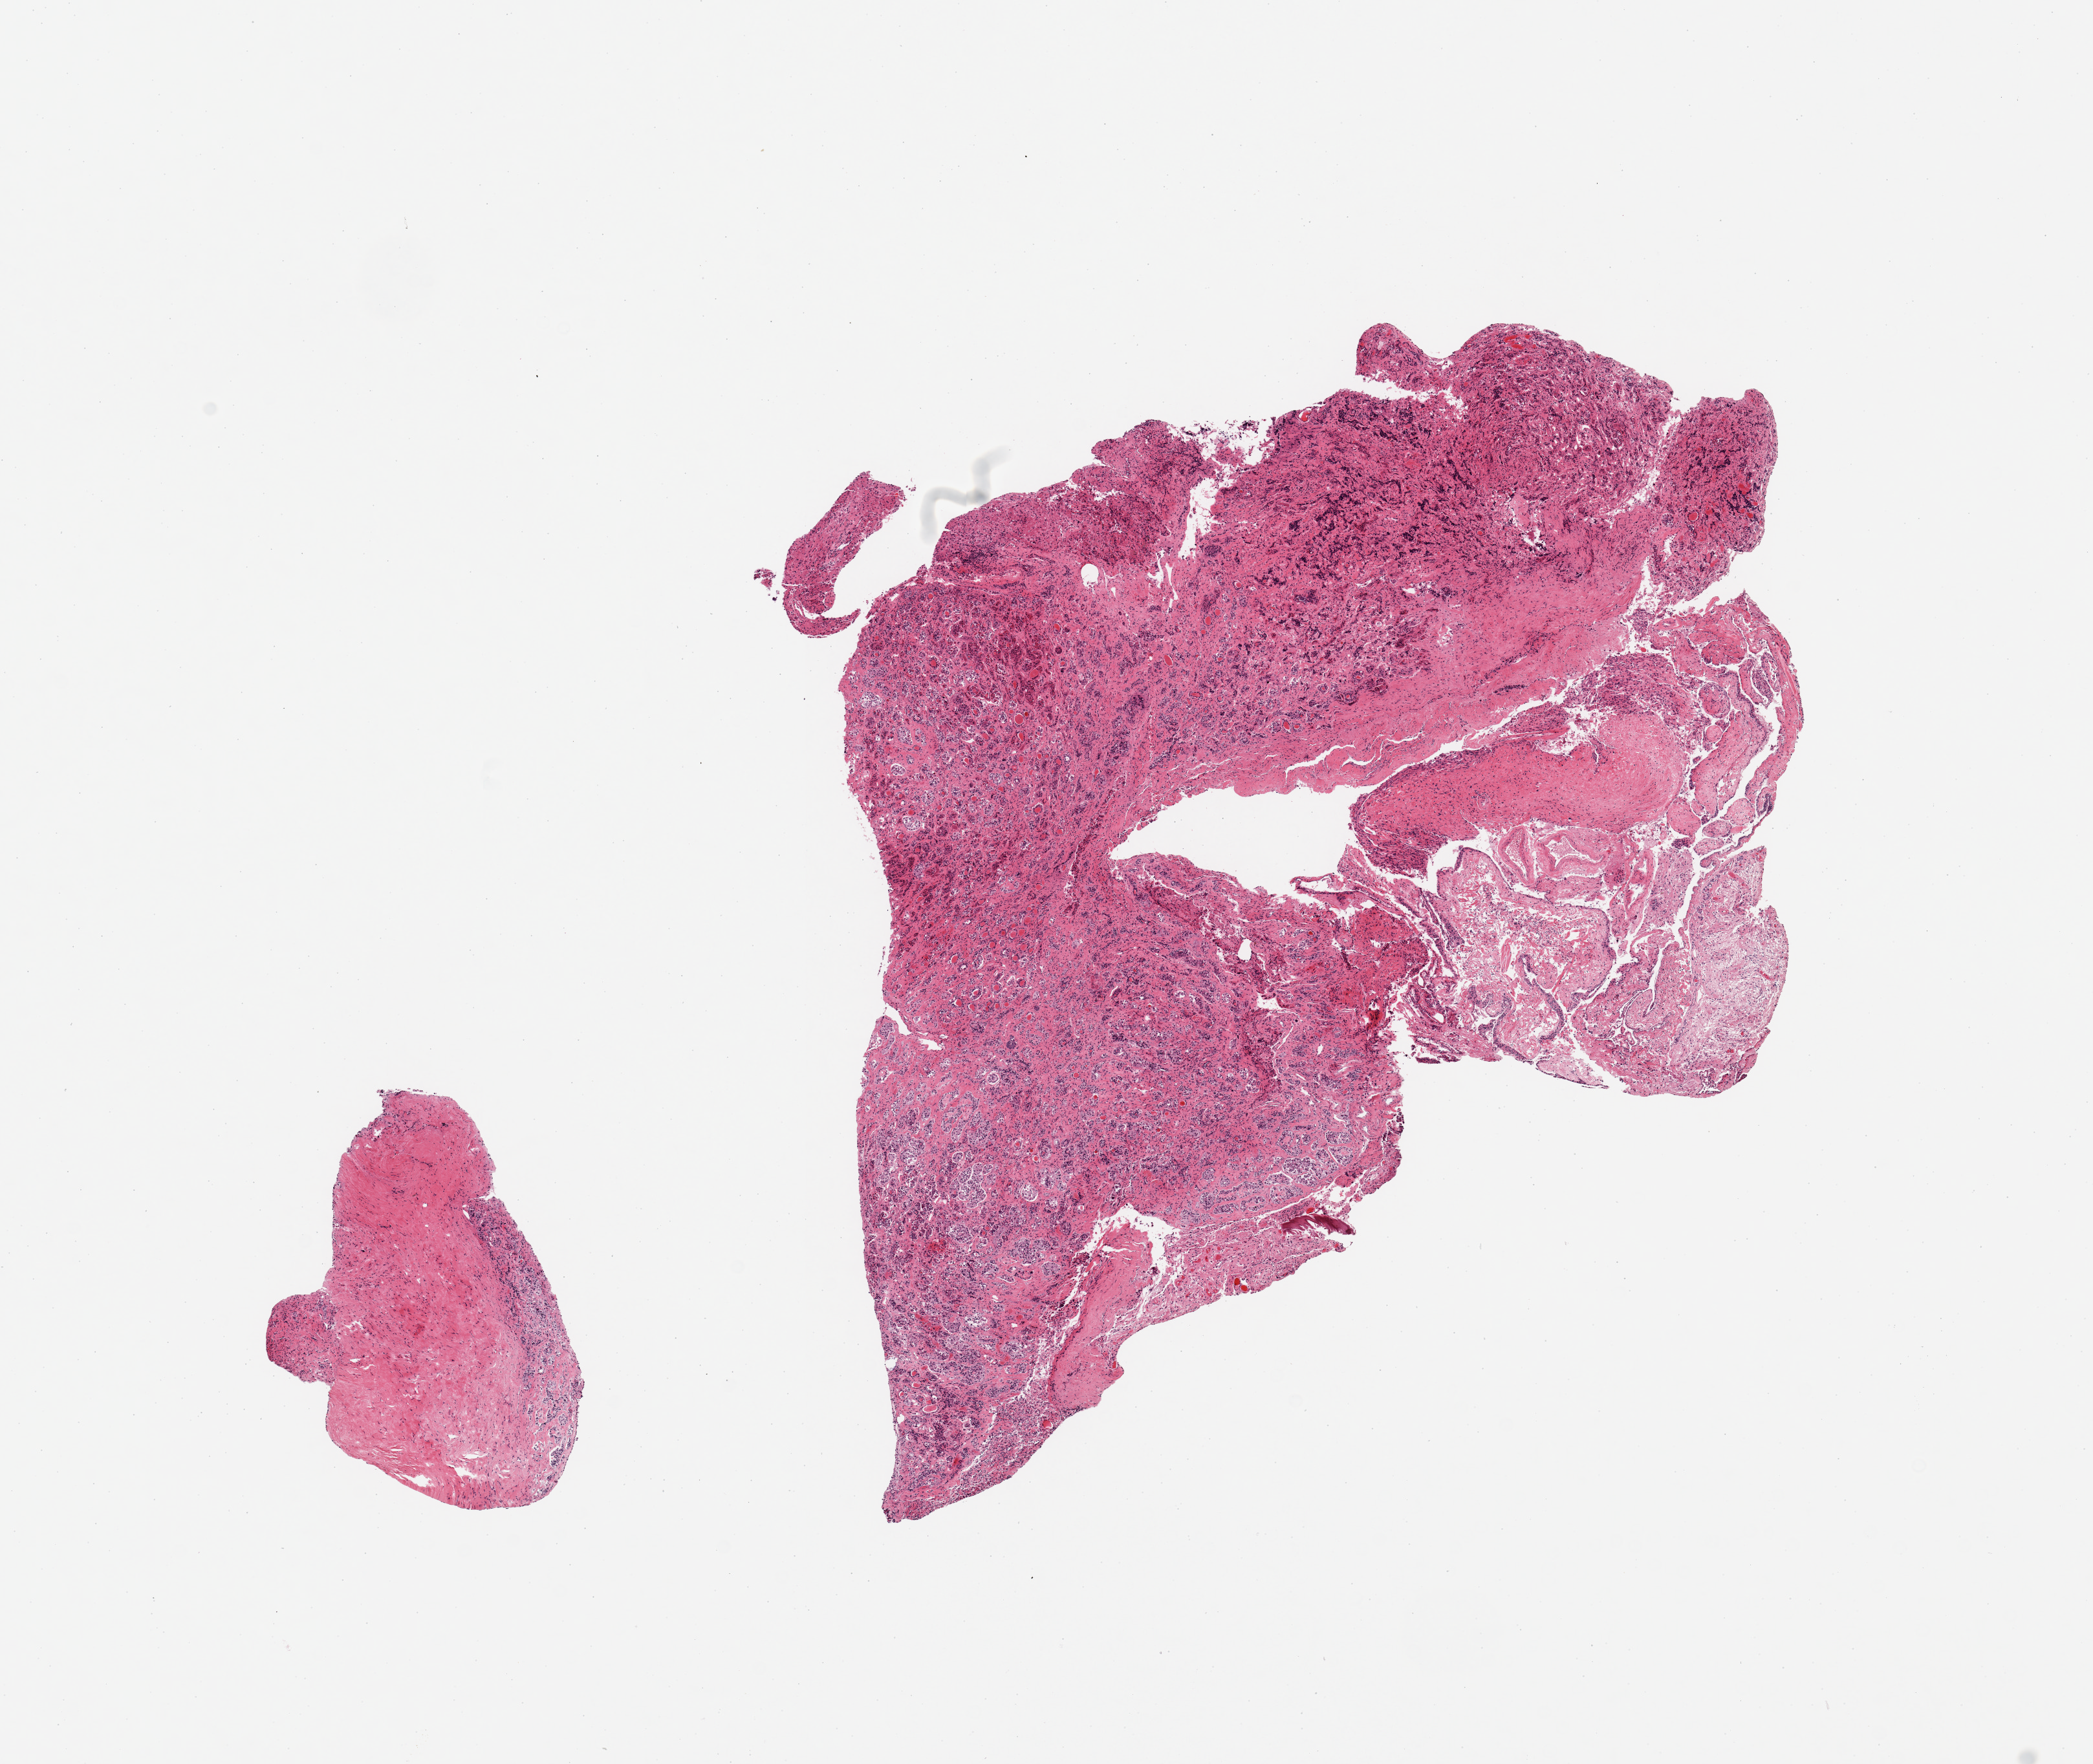
Digitized hematoxylin and eosin (H&E)-stained section, shown as a low-resolution overview of the whole scanned area (about 12.8 x 10.8 mm, from a 20x scan), PAXgene-fixed, paraffin-embedded tissue, section of pituitary (target tissue), donor tissue sample. Donor: male.
- reviewer comment on this tissue sample: 1 piece; small amounts of anterior, posterior & intermediate plus a fibrous fragment; too little target tissues for adequate study